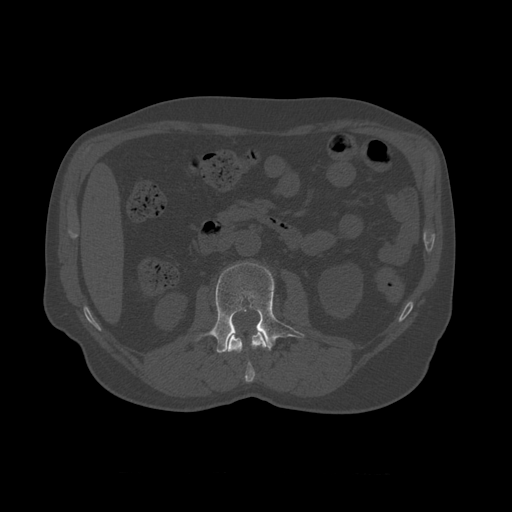
CT including the spine, one axial slice. Position 335 of 450 along the scan axis. Reconstruction kernel STANDARD. Bone window (W 1800 / L 400 HU). 1.25 mm slice thickness. 512 × 512 image matrix, field of view 405 × 405 mm. Patient age 75 years. Case-level facts recorded for this patient, not image findings: primary cancer: prostate.
Outlined on this slice (semi-automatic segmentation, software-assisted and operator-edited):
- L1 vertebra: box from (x=227, y=330) to (x=268, y=383) px
- L2 vertebra: (x=196, y=263)–(x=305, y=353)